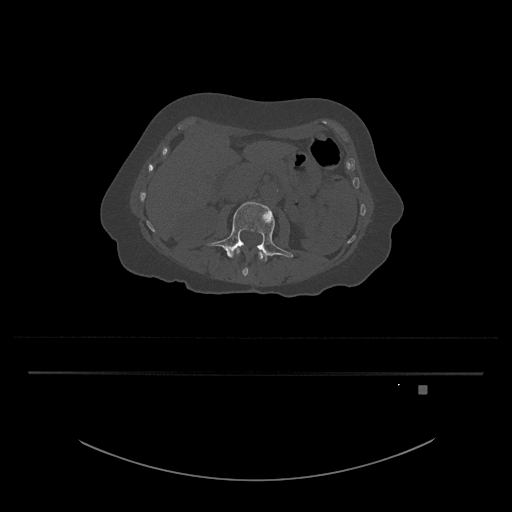
CT including the spine, one axial slice; position 440 of 797 along the scan axis; reconstruction kernel Br40s/3; 120 kVp; bone window (W 1800 / L 400 HU); 512 × 512 image matrix, field of view 500 × 500 mm. Patient: female, 57 years. Case-level facts recorded for this patient, not image findings: primary cancer: cervical.
Structures marked on this image (semi-automatically segmented with operator editing):
- L3 vertebra: bounding box <207,201,293,262> (left, top, right, bottom; pixels)